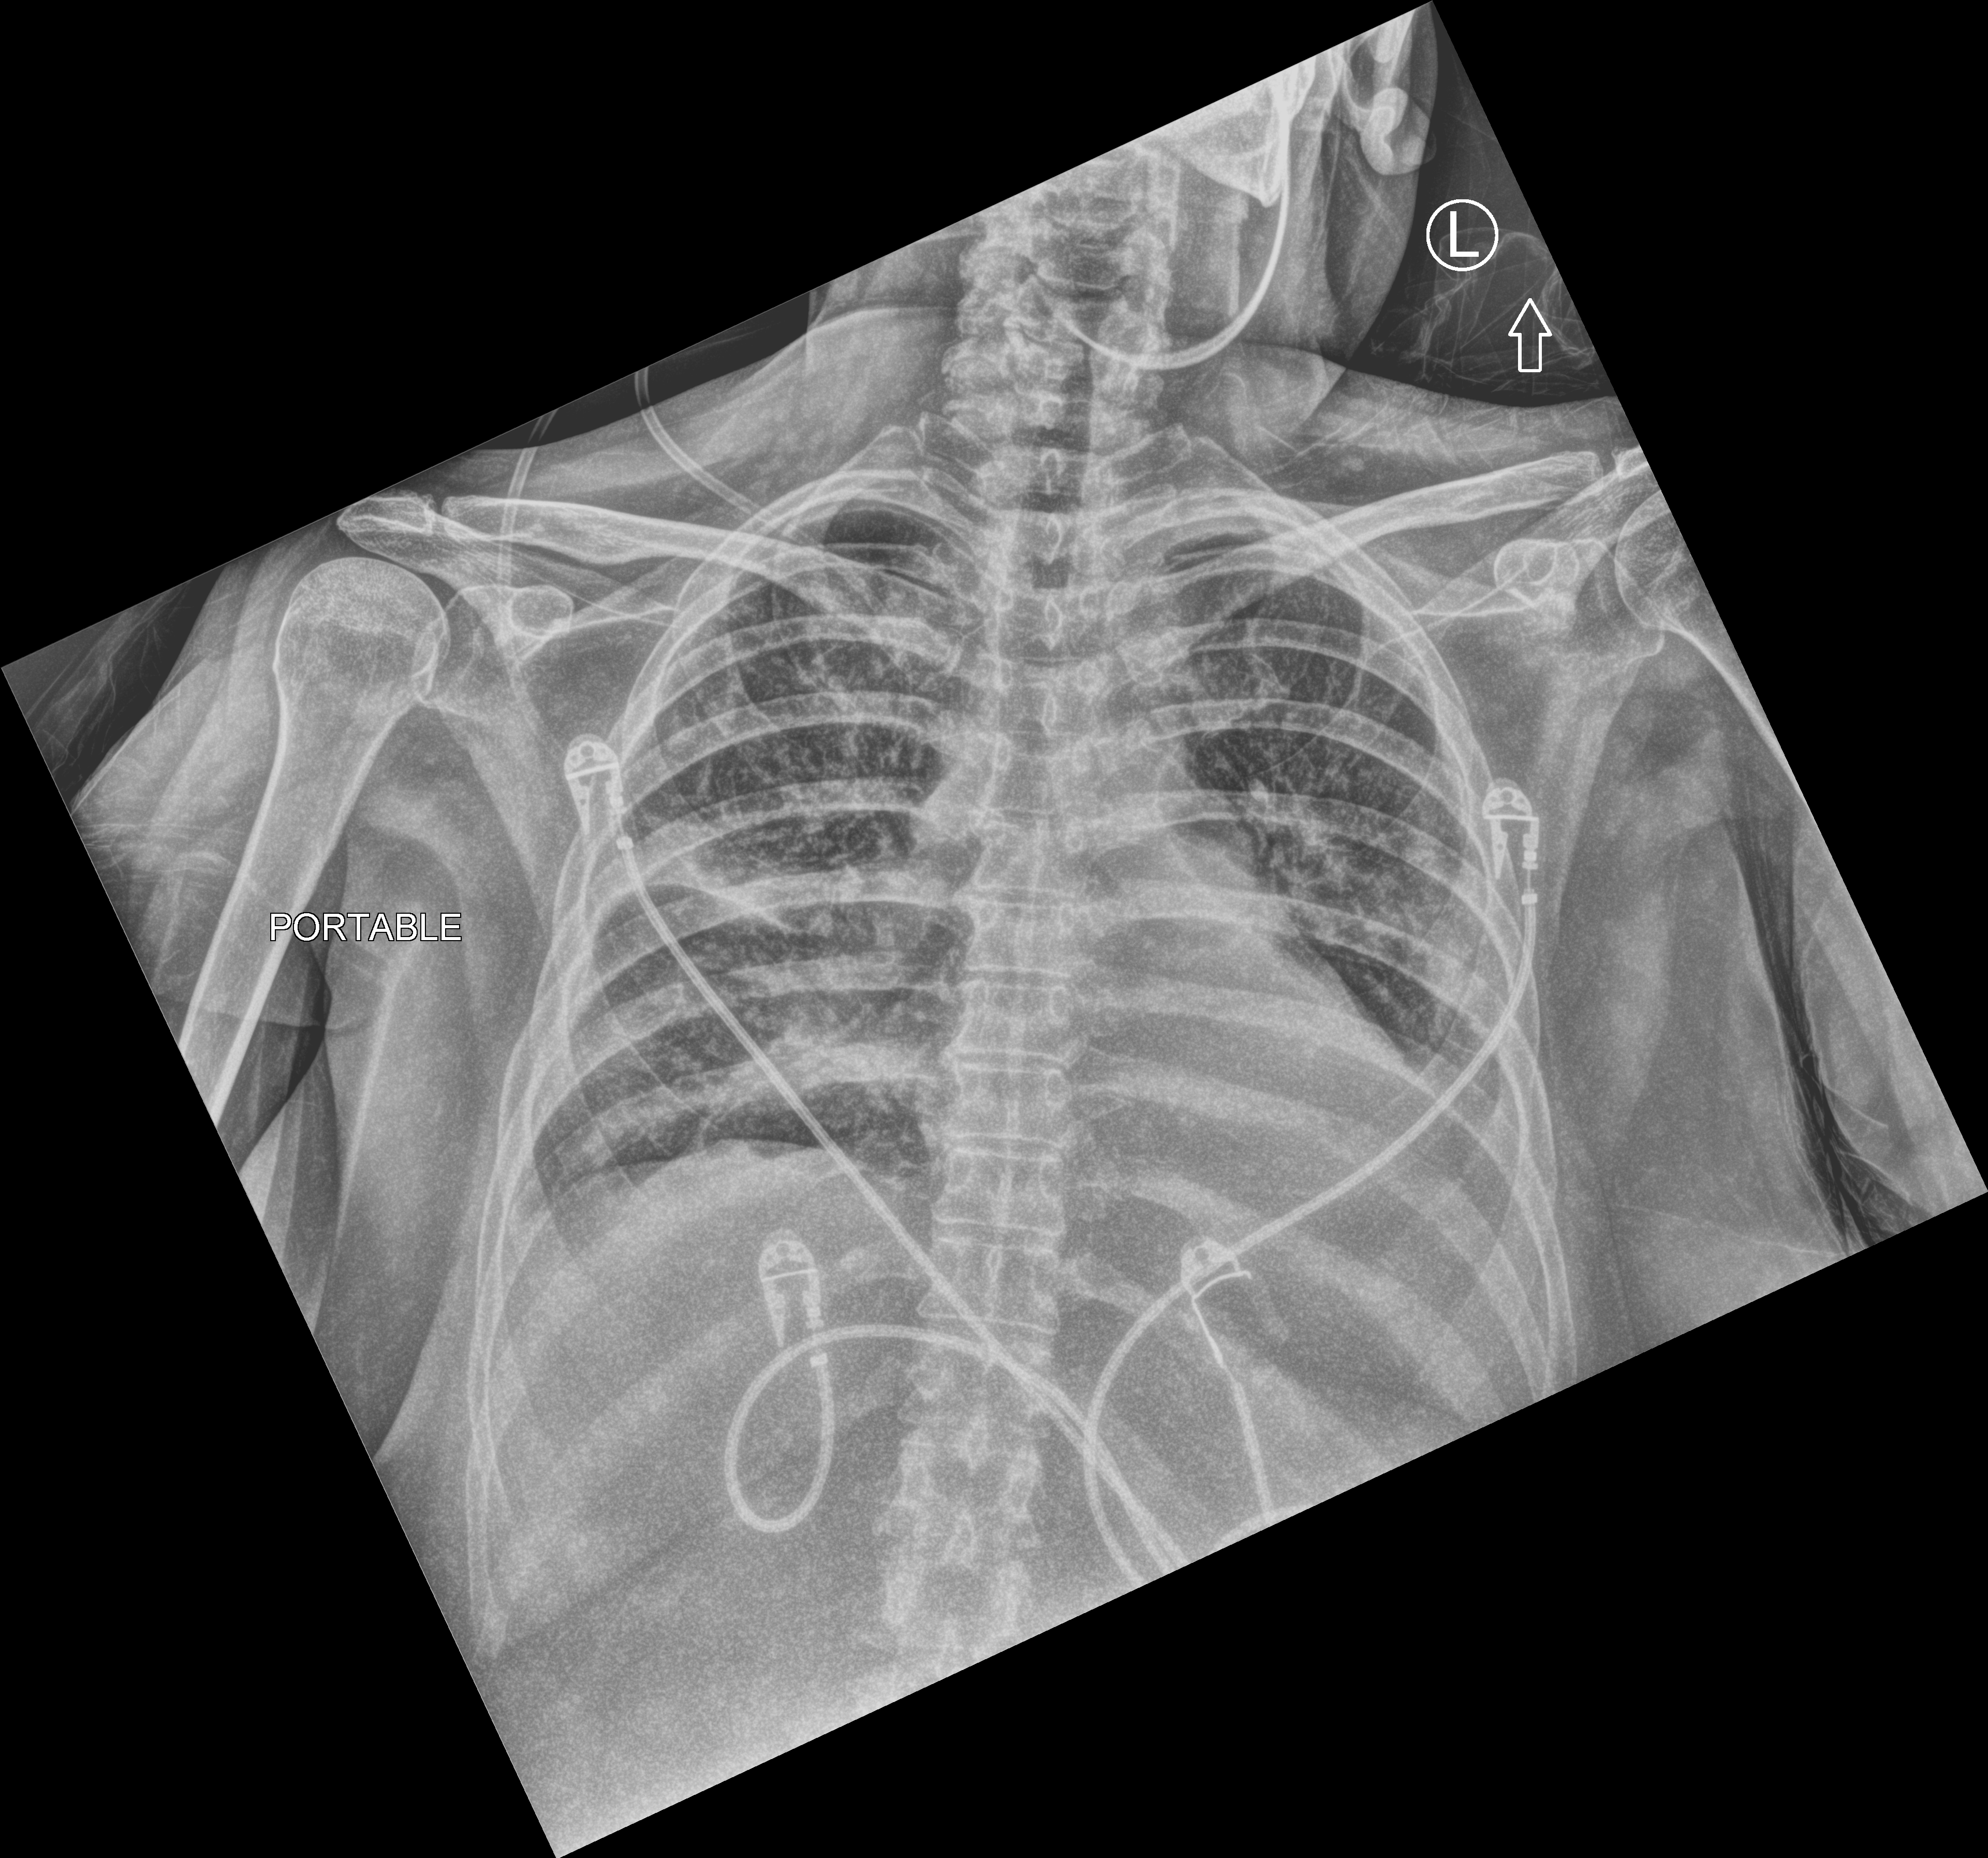
Portable chest radiograph; anteroposterior (AP) projection. Patient hospitalised with COVID-19; female, aged 60–74 years.
Hospital-stay facts (about this admission, not read from this image; timing relative to this image not recorded): mechanically ventilated during this hospital stay: yes; admitted to intensive care during this hospital stay: yes.